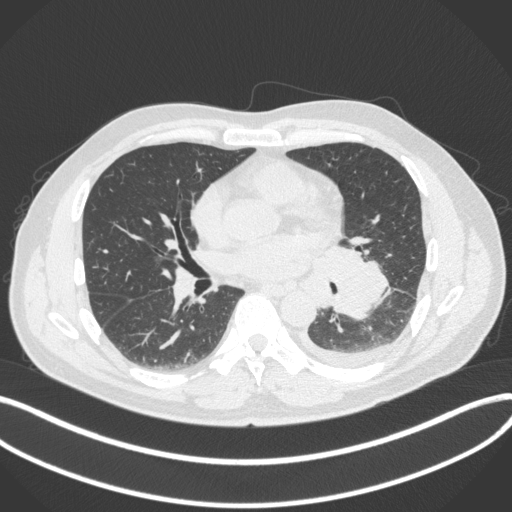
Chest CT, one axial slice; 120 kVp; lung window (W 1500 / L -600 HU); 1 mm slice thickness; 512 × 512 image matrix, field of view 400 × 400 mm. Patient: male, 58 years. From the clinical record (not read from this slice): clinical TNM (as recorded): T3 N1 M1b.
Structures marked on this image (bounding box drawn by a radiologist):
- lung tumour (recorded histology: small cell carcinoma): bounding box [x1, y1, x2, y2] px = [310, 233, 395, 321]